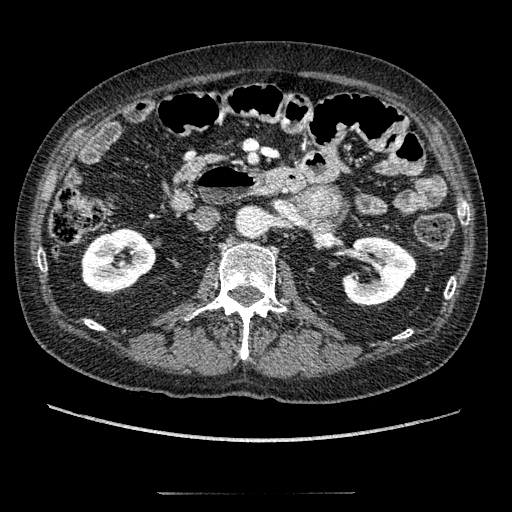
Contrast-enhanced abdominal CT, one axial slice; slice 84 of 274 in the series (ordered by position); soft-tissue window (W 400 / L 40 HU); 1.25 mm slice thickness; 512 × 512 image matrix, field of view 381 × 381 mm. Patient: male, 69 years. Case-level facts recorded for this patient, not image findings: diagnosis: adrenocortical carcinoma; tumour side: left adrenal; tumour size at pathology: 6.1 cm; Ki-67 index: 10 %; stage (as recorded): 3.
Structures marked on this image (semi-automatically segmented with operator editing):
- mass: bounding box <297,185,347,218> (left, top, right, bottom; pixels)